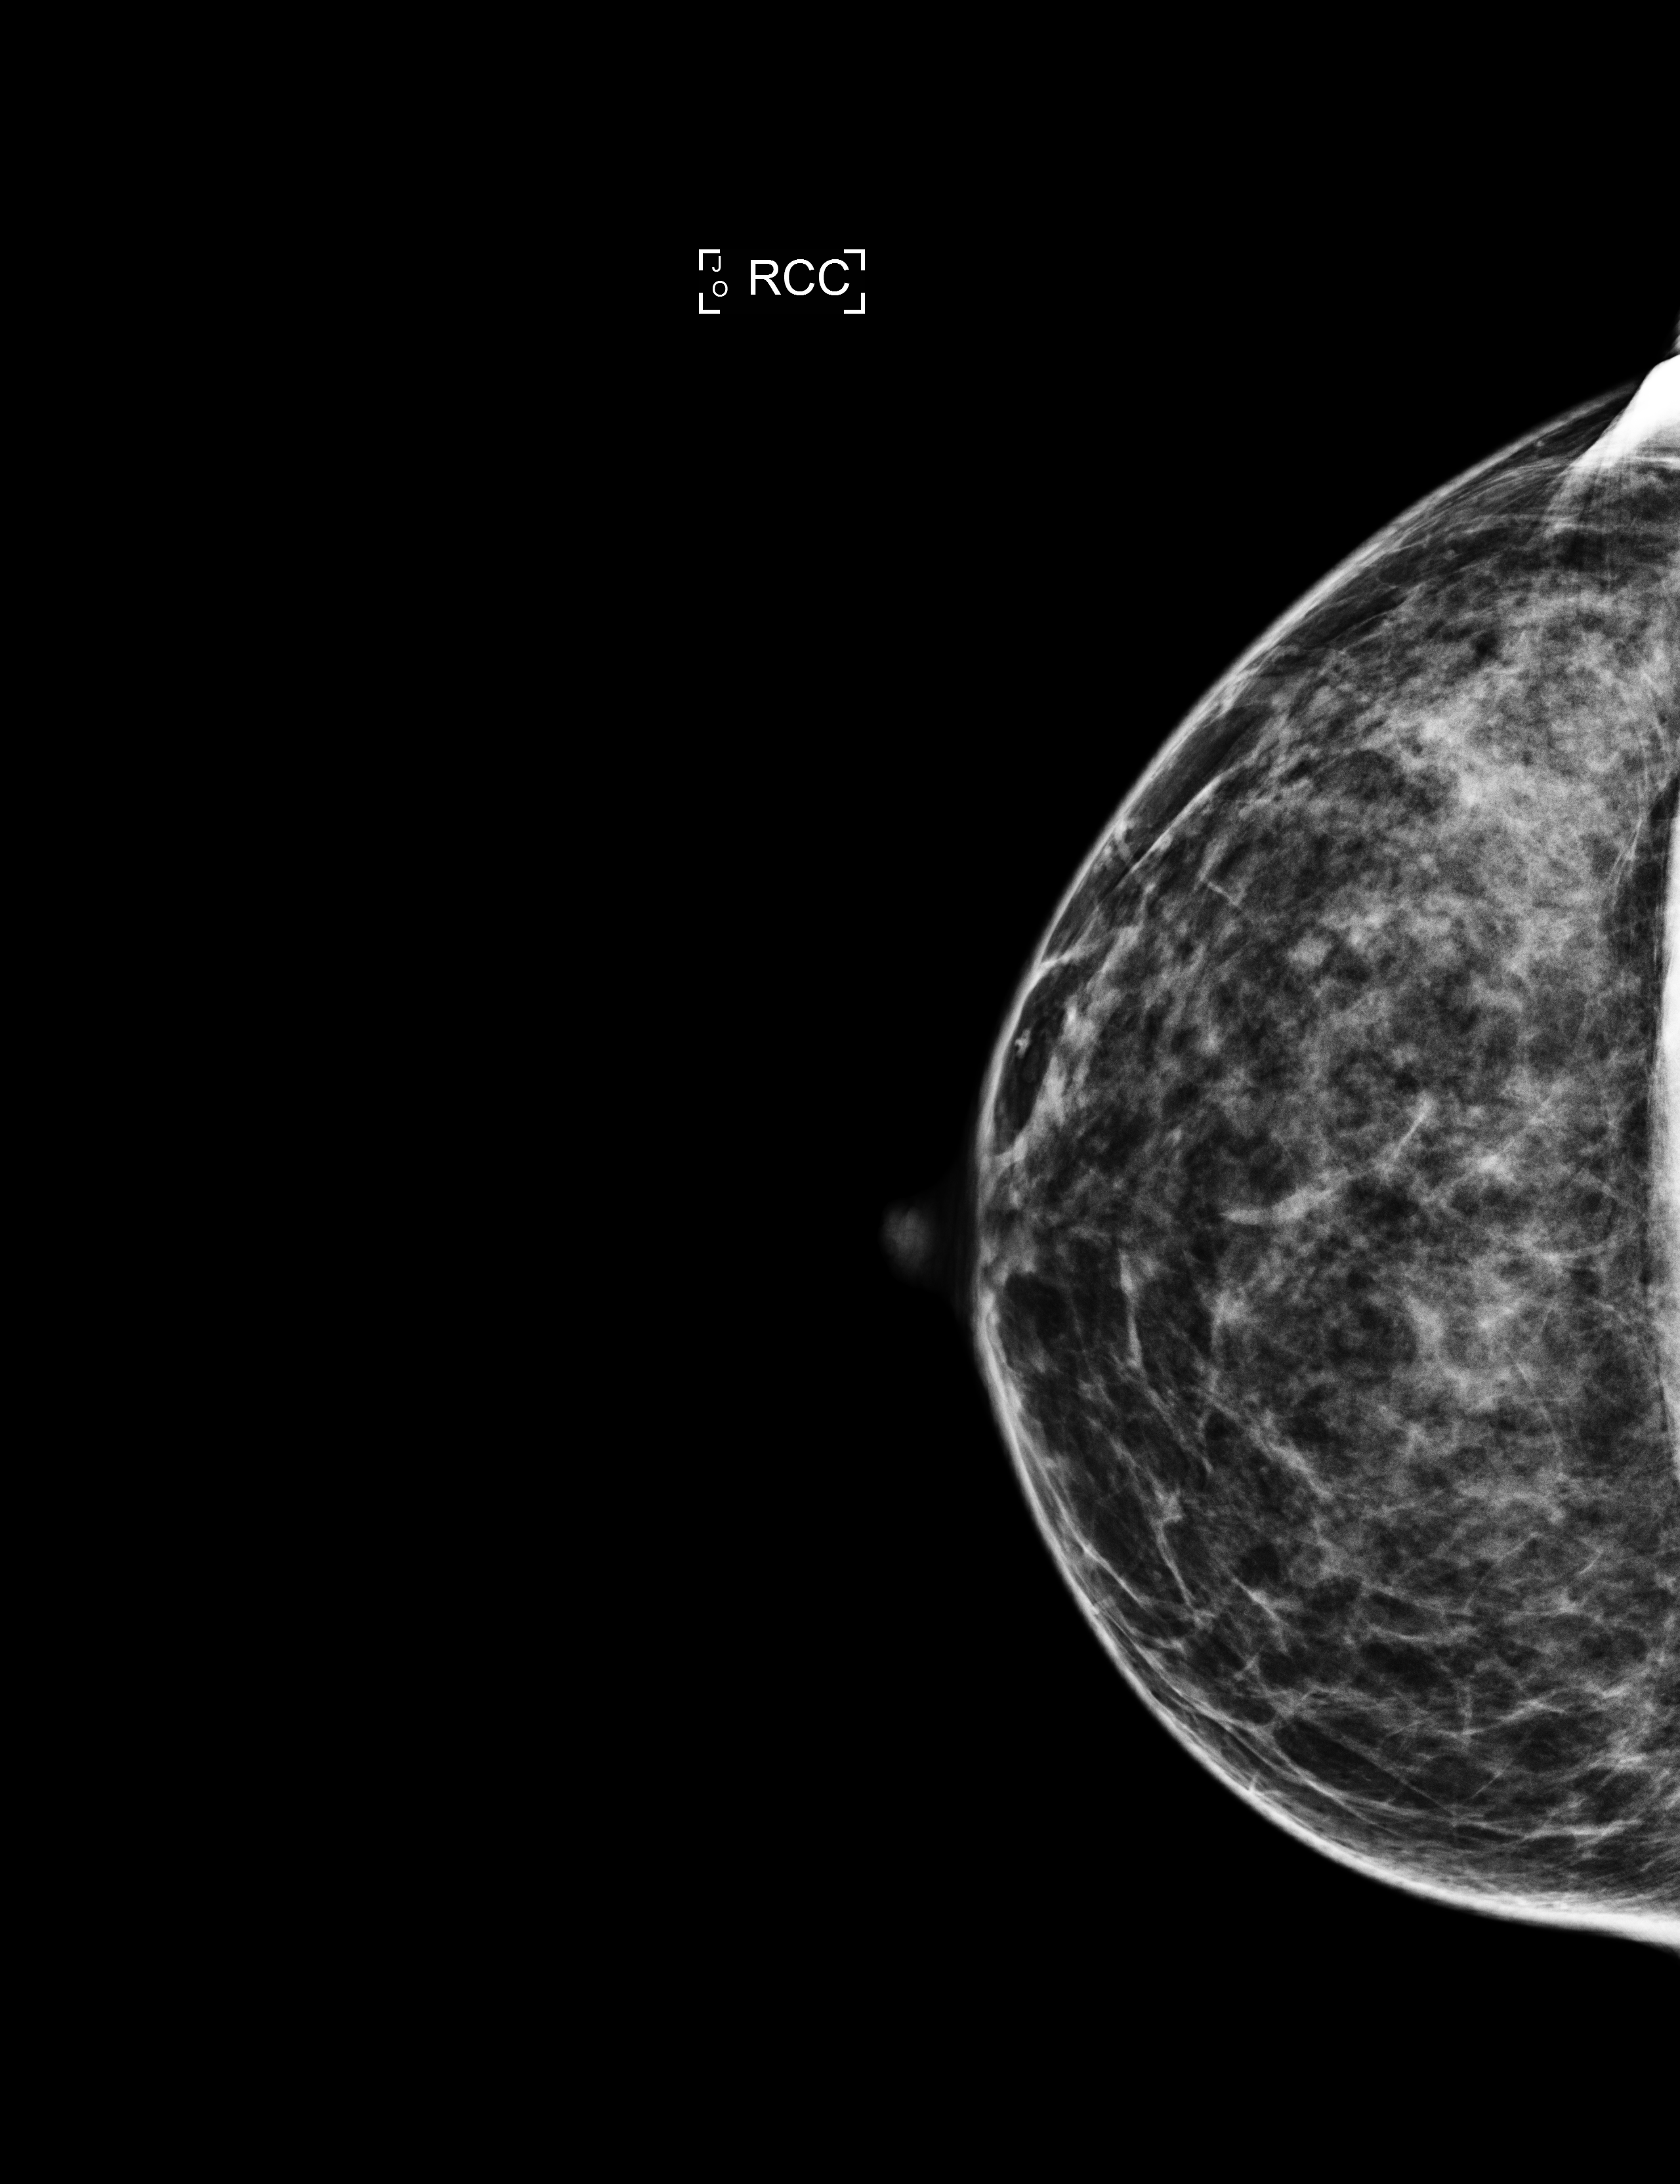
Digital mammogram (FFDM); right breast; CC view; screening examination; compressed breast thickness 58 mm; system: Selenia Dimensions. Female patient, age 41 years.
- breast density at the screening exam (both breasts): heterogeneously dense (BI-RADS density category c)
- final BI-RADS assessment for this screening round (tomosynthesis exam, both breasts): category 1
- recall: no recall after this screen